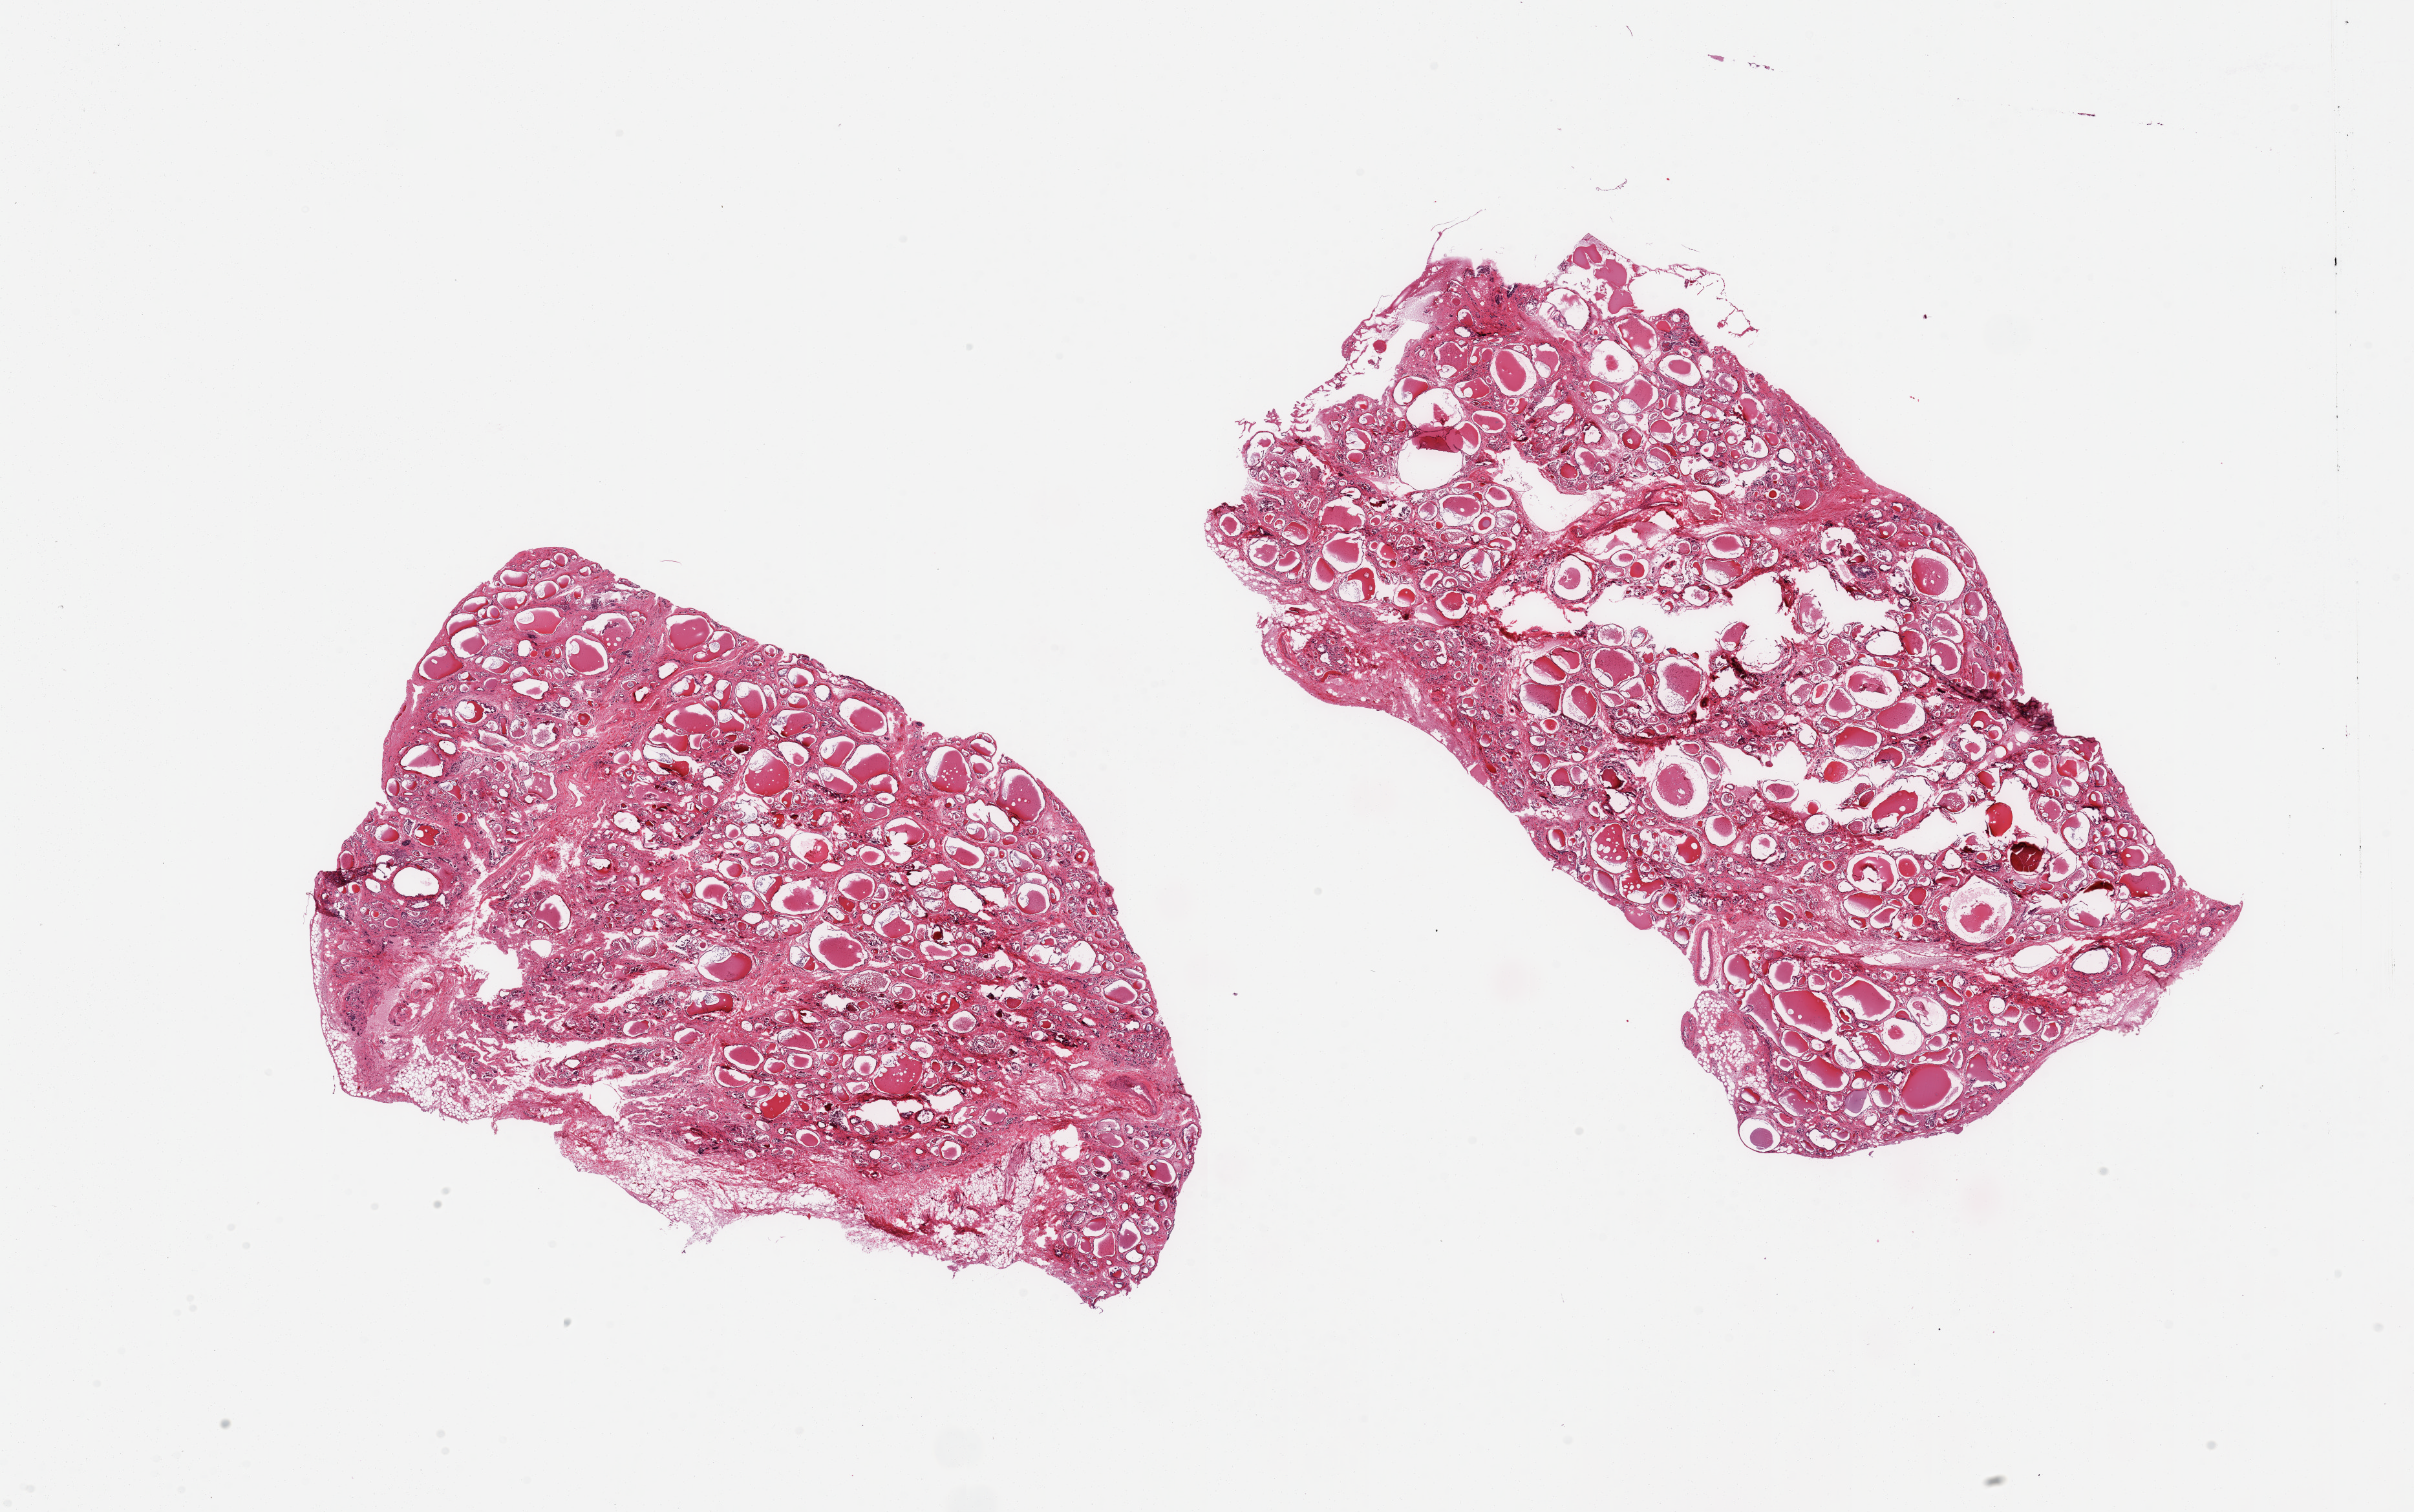
H&E whole-slide image — shown as a low-resolution overview of the whole scanned area (about 29.5 x 18.5 mm, acquisition: 20x scan). PAXgene-fixed, paraffin-embedded tissue. Section of thyroid (target tissue). Tissue donor sample. Donor: male.
- pathologist's review note for this sample: 2 pieces, regressive changes; adherent nubbins of fat up to ~1.5mm